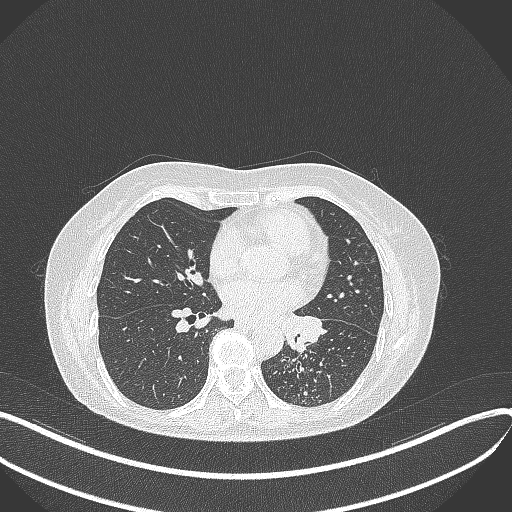
Chest CT, one axial slice. Reconstruction kernel B70f. 100 kVp. Lung window (W 1500 / L -600 HU). 1 mm slice thickness. 512 × 512 image matrix, field of view 400 × 400 mm. Female patient, age 63 years. From the clinical record (not read from this slice): clinical TNM (as recorded): T1b N0 M0.
Annotated regions visible in this slice (bounding box drawn by a radiologist):
- lung tumour (recorded histology: adenocarcinoma): bounding box [x1, y1, x2, y2] px = [277, 306, 330, 353]